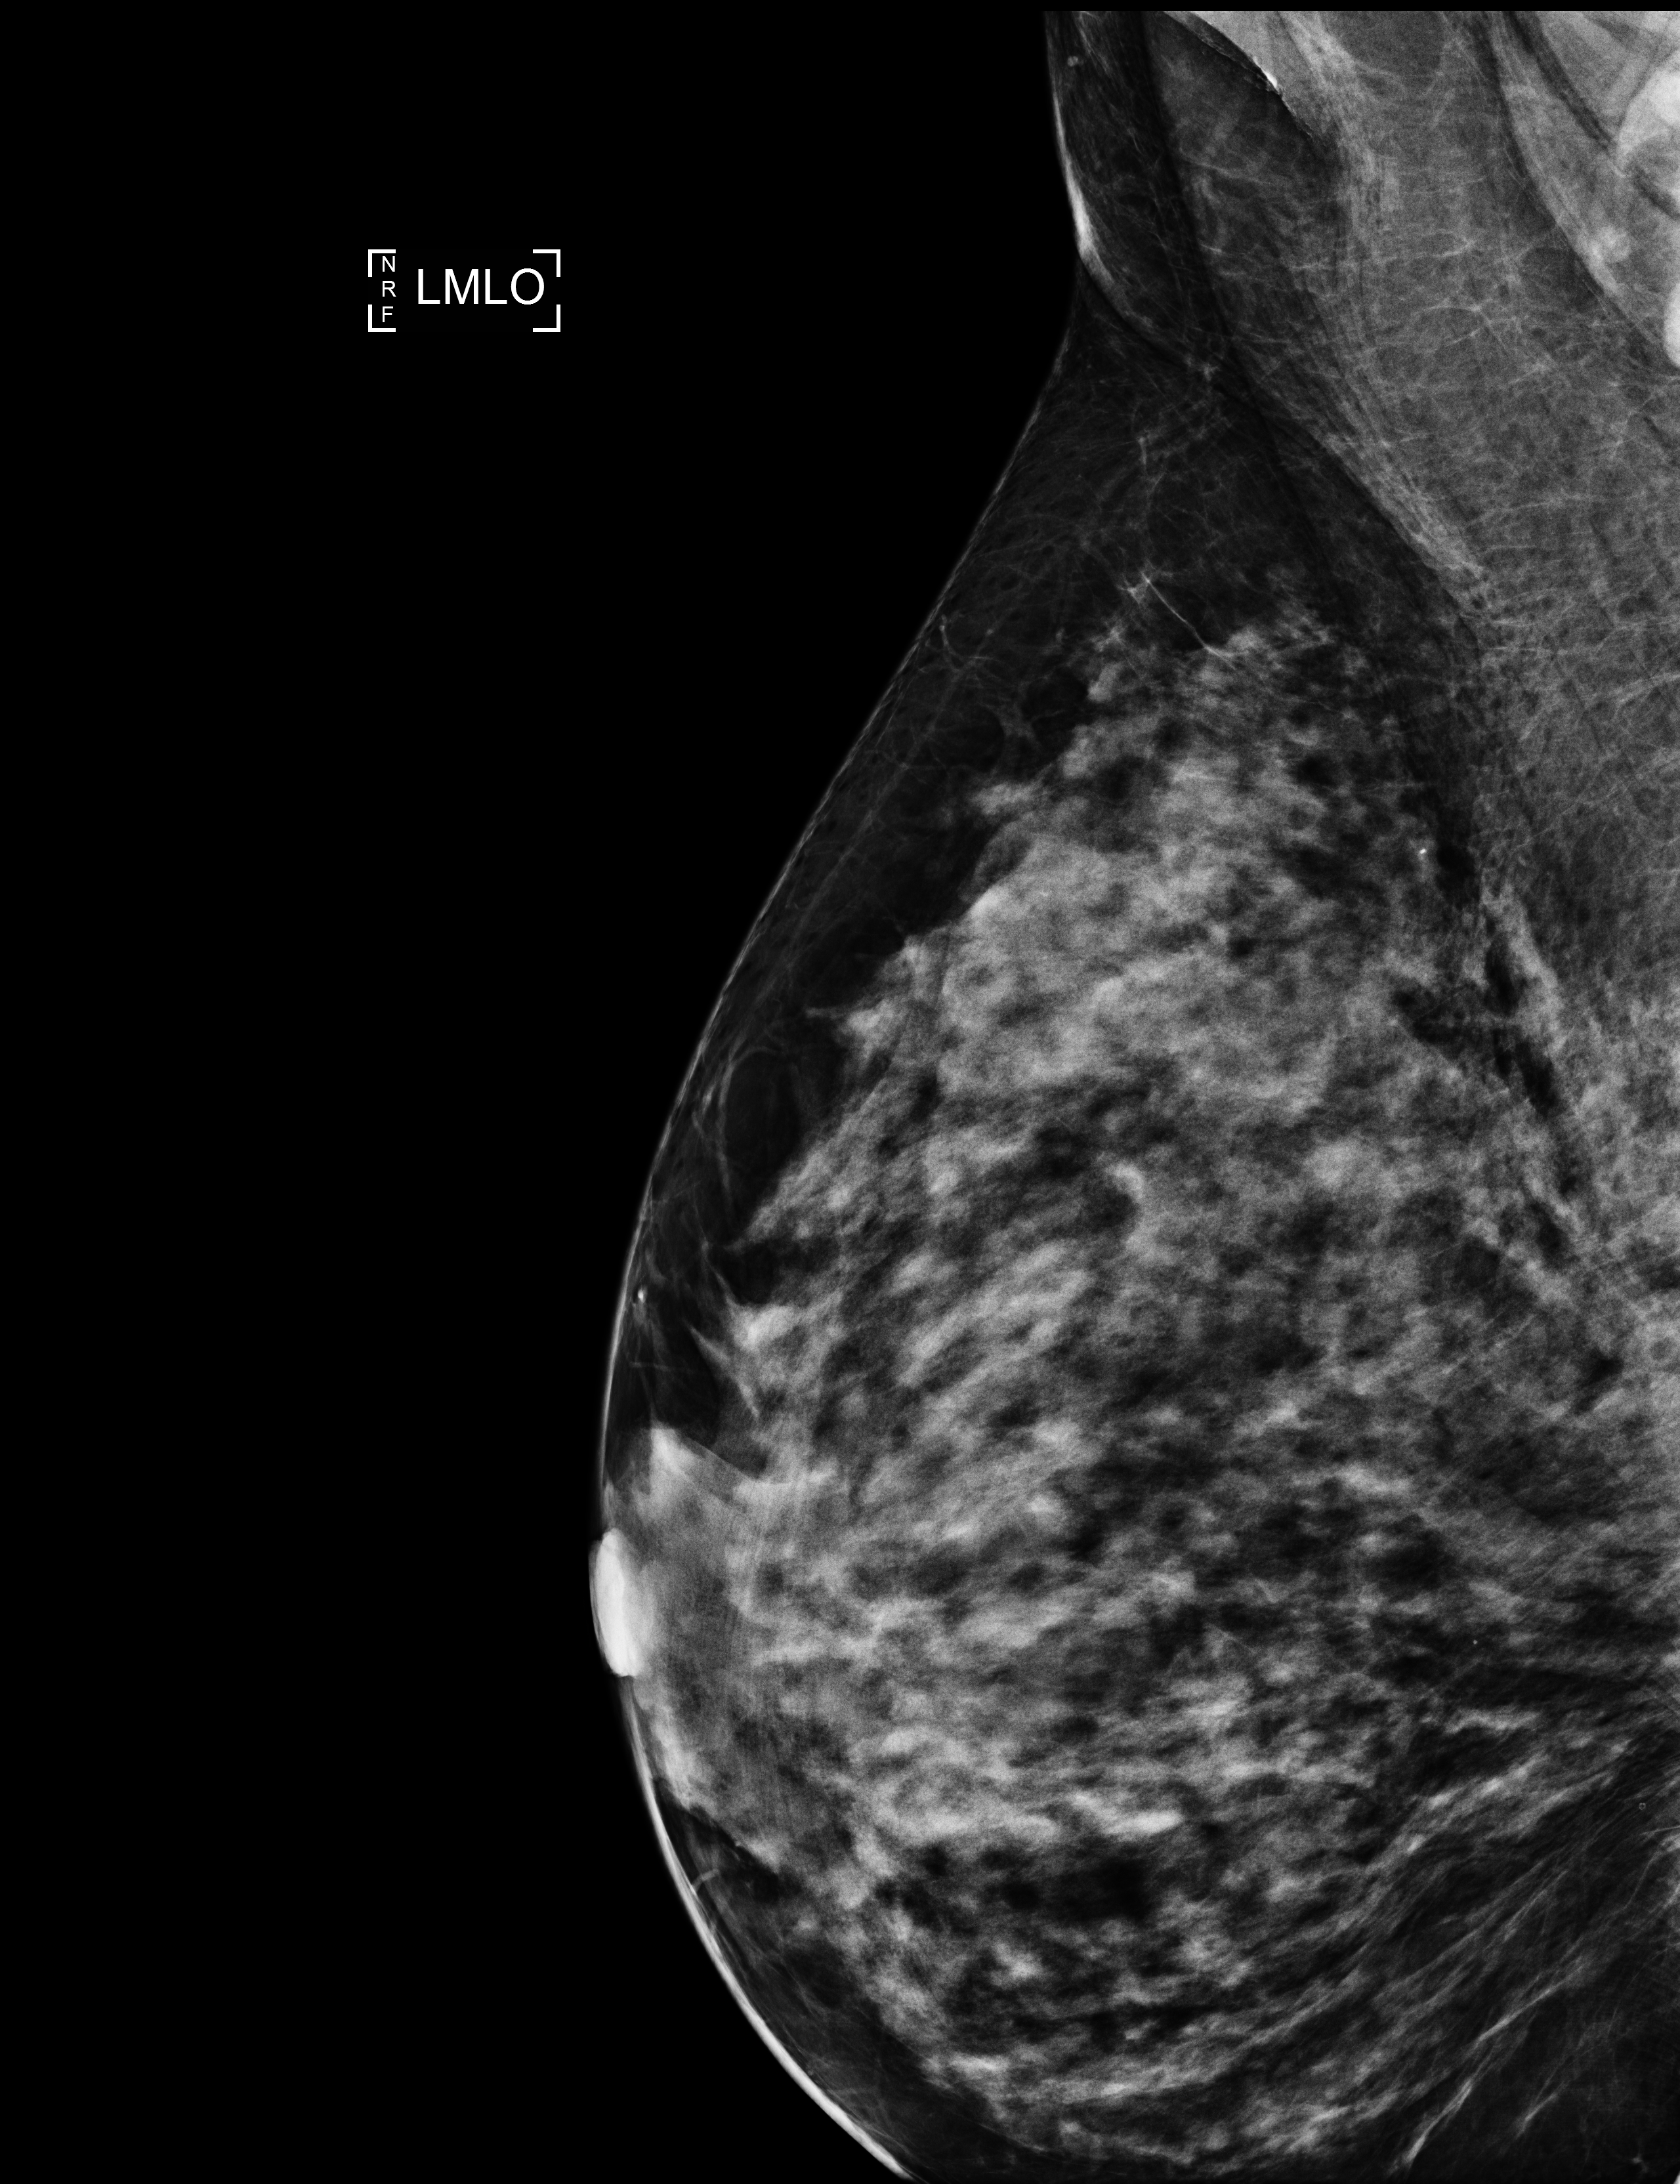
Screening examination; system: Selenia Dimensions. Patient: female, 60 years.
Image type: full-field digital mammogram. Breast: left. Projection: medio-lateral oblique projection. Breast density at the screening exam (both breasts): extremely dense (BI-RADS density category d). Final BI-RADS assessment for this screening round (tomosynthesis exam, both breasts): category 1. Recall: no recall after this screen.